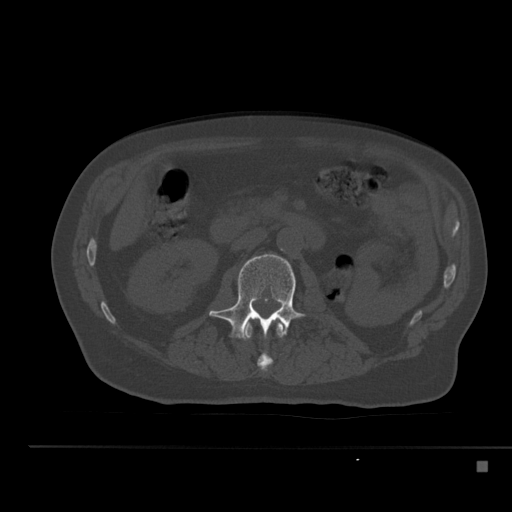
CT including the spine, one axial slice. Position 188 of 517 along the scan axis. Bone window (W 1800 / L 400 HU). 1.5 mm slice thickness. 512 × 512 image matrix, field of view 408 × 408 mm. Patient: male, 70 years. From the clinical record (not read from this slice): primary cancer: renal; vertebrae with lytic lesions (as recorded): T4, T6, T10, T12, L3, L4, L5.
Structures marked on this image (semi-automatic segmentation, software-assisted and operator-edited):
- L1 vertebra: bounding box [x1, y1, x2, y2] px = [242, 319, 286, 372]
- L2 vertebra: [209, 254, 306, 338]